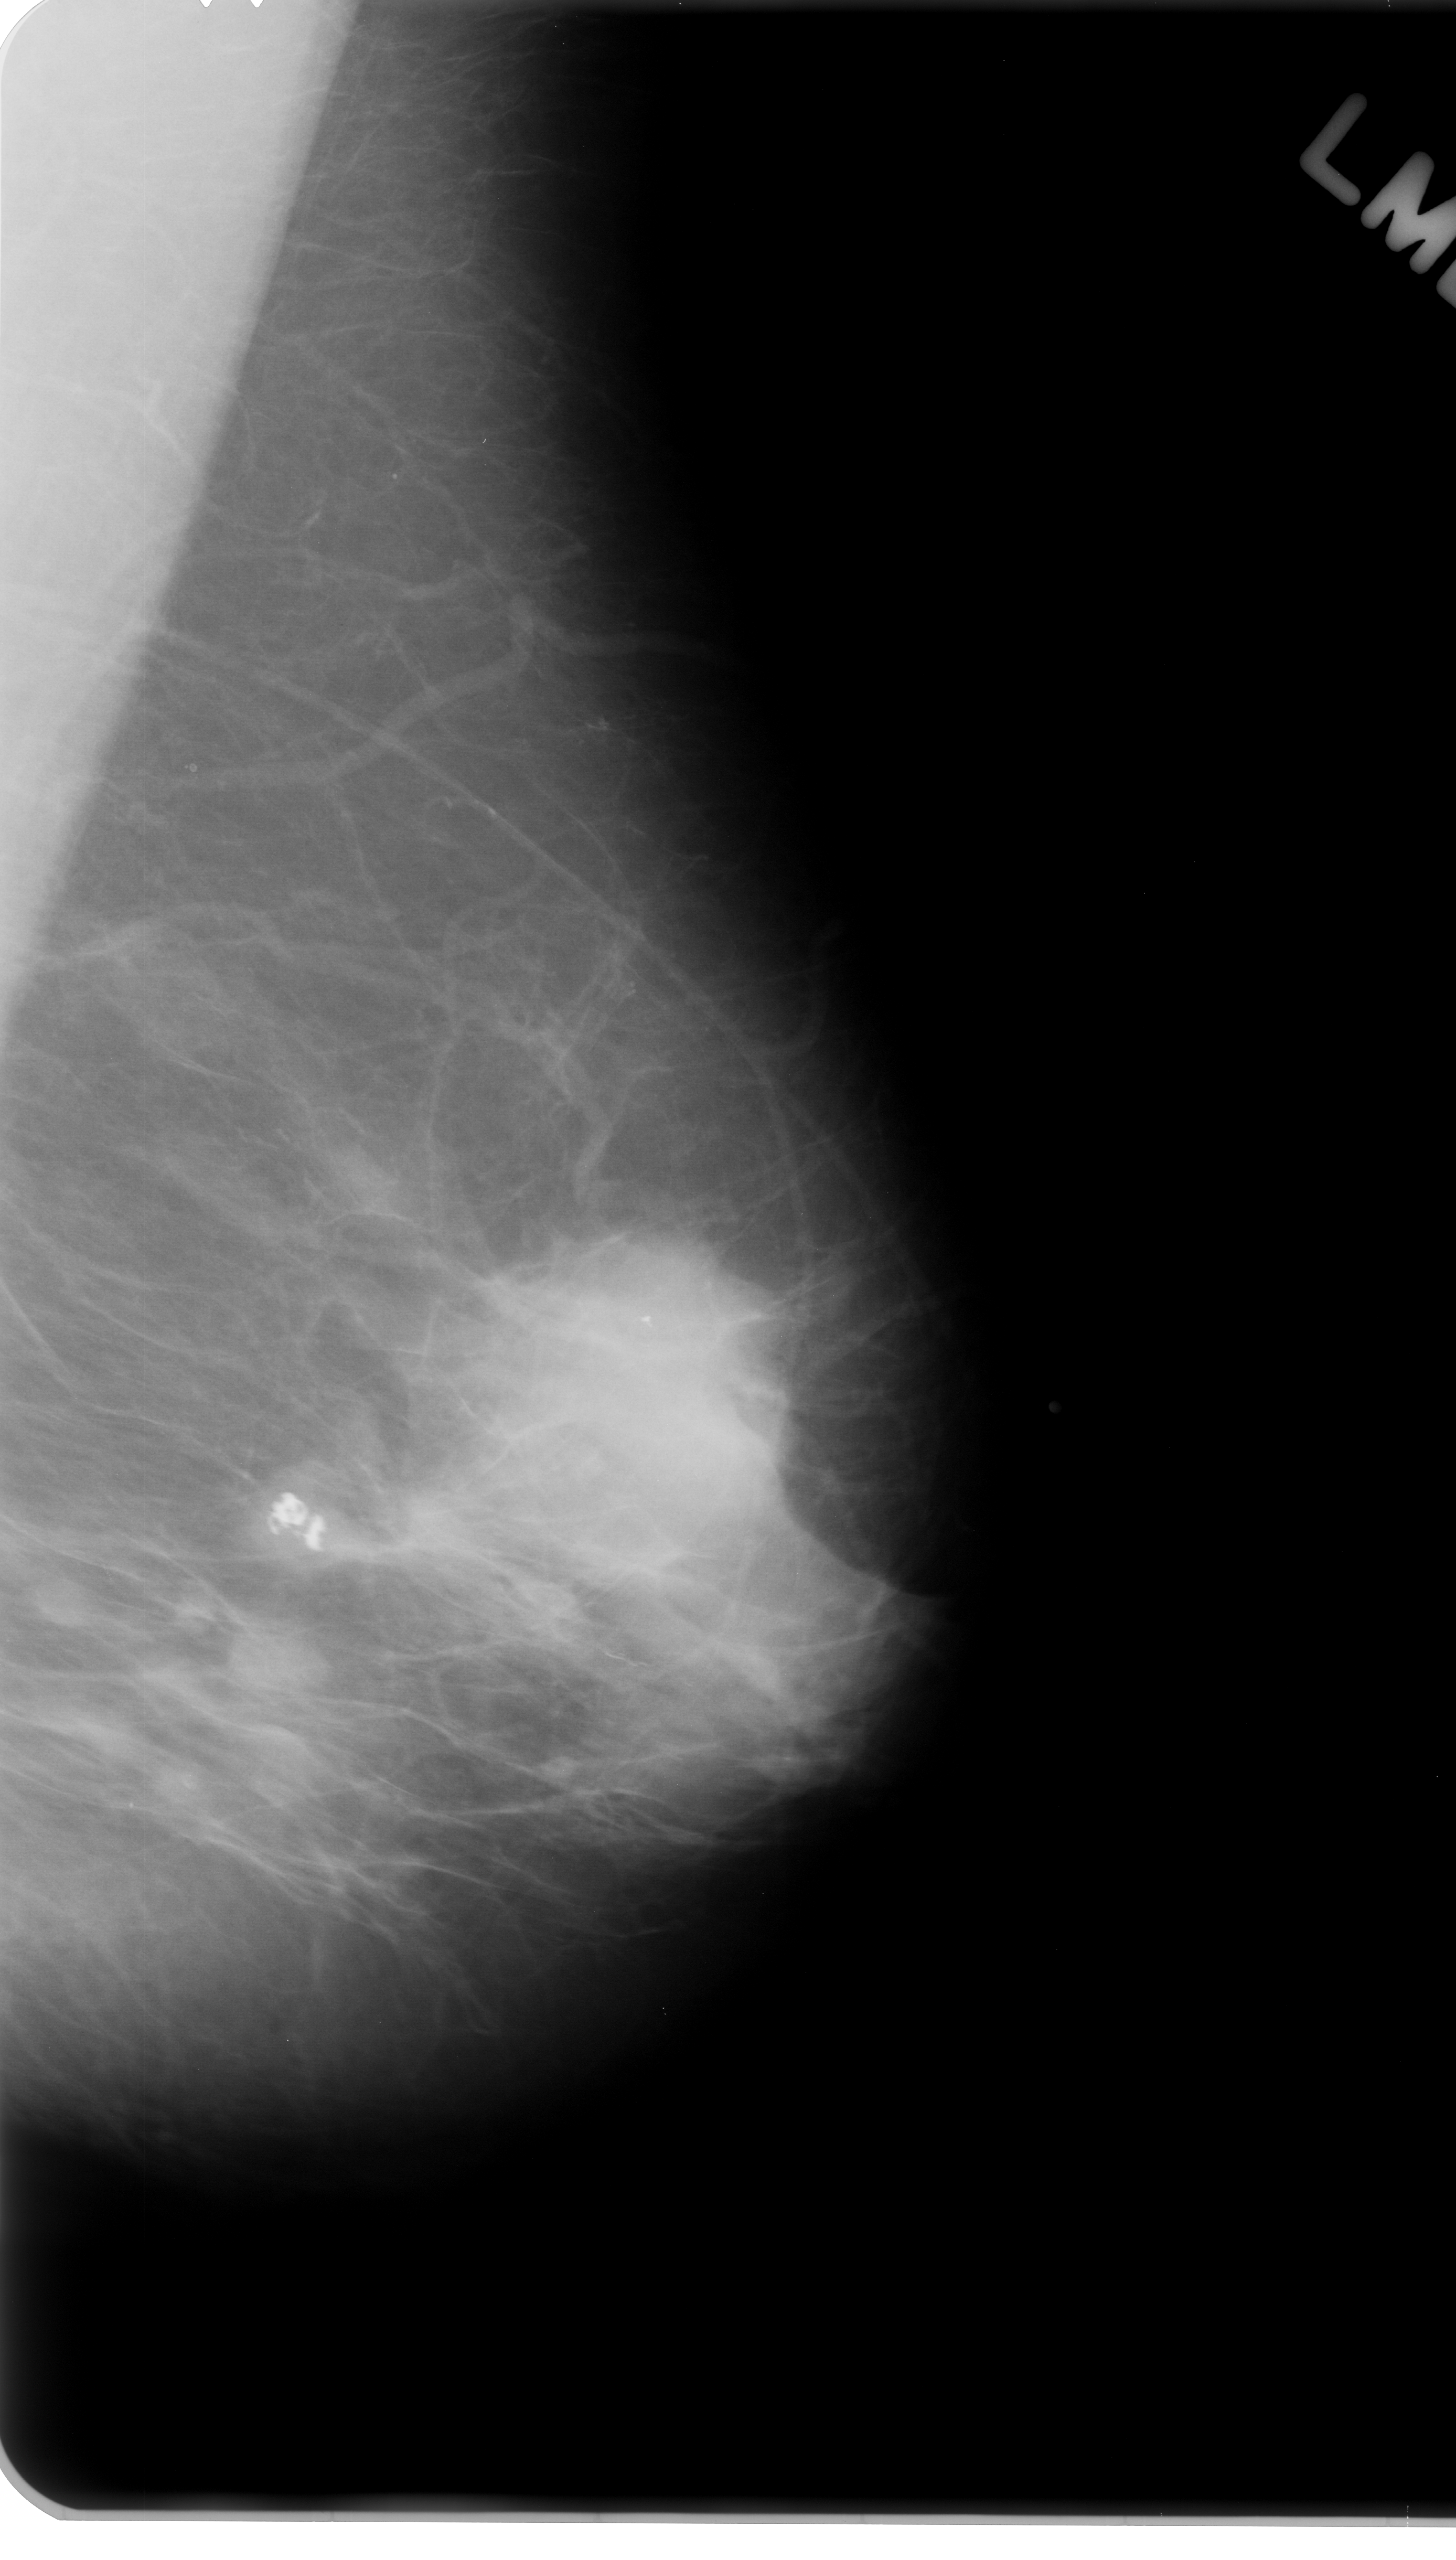
Mammogram (digitized film); left breast; MLO view; BI-RADS breast density category 2 (scale 1–4).
Mass, shape round, margins ill defined; BI-RADS assessment category 4; subtlety rating 5 on a 1 (subtle) to 5 (obvious) scale; pathology (as recorded): malignant.